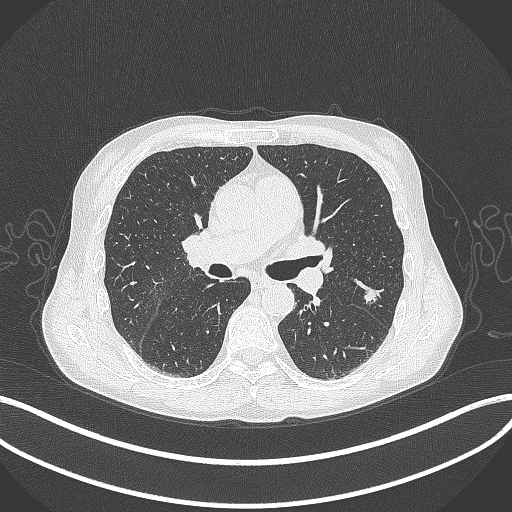
Chest CT, one axial slice; position 211 of 429 along the scan axis; 120 kVp; lung window (W 1500 / L -600 HU); 512 × 512 image matrix, field of view 400 × 400 mm. Patient: male, 58 years. Case-level facts recorded for this patient, not image findings: clinical TNM (as recorded): T1c N0 M0.
Outlined on this slice (bounding box drawn by a radiologist):
- lung tumour (recorded histology: adenocarcinoma): bounding box <362,284,380,305> (left, top, right, bottom; pixels)